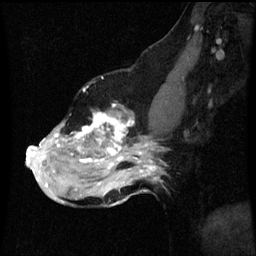
Breast MRI (dynamic contrast-enhanced), one sagittal slice; position 36 of 60 along the scan axis; dynamic contrast-enhanced series, image 2 of 3 at this slice position (ordered by acquisition); 1.5 T; TE 4.2 ms, TR 8.9 ms; 2 mm slice thickness; 256 × 256 image matrix, field of view 200 × 200 mm. Female patient, age 49 years. From the clinical record (not read from this slice): setting: breast cancer imaged before/during neoadjuvant chemotherapy; receptor status: HR-positive, HER2-negative.
Outlined on this slice (semi-automatic segmentation, software-assisted and operator-edited):
- analysis volume of interest (the breast-tissue region the enhancement analysis was run in; not a lesion): box from (x=28, y=106) to (x=159, y=199) px
- tumour enhancement mask (voxels above the 70 % enhancement threshold inside the analysis volume of interest): (x=28, y=106)–(x=157, y=187)